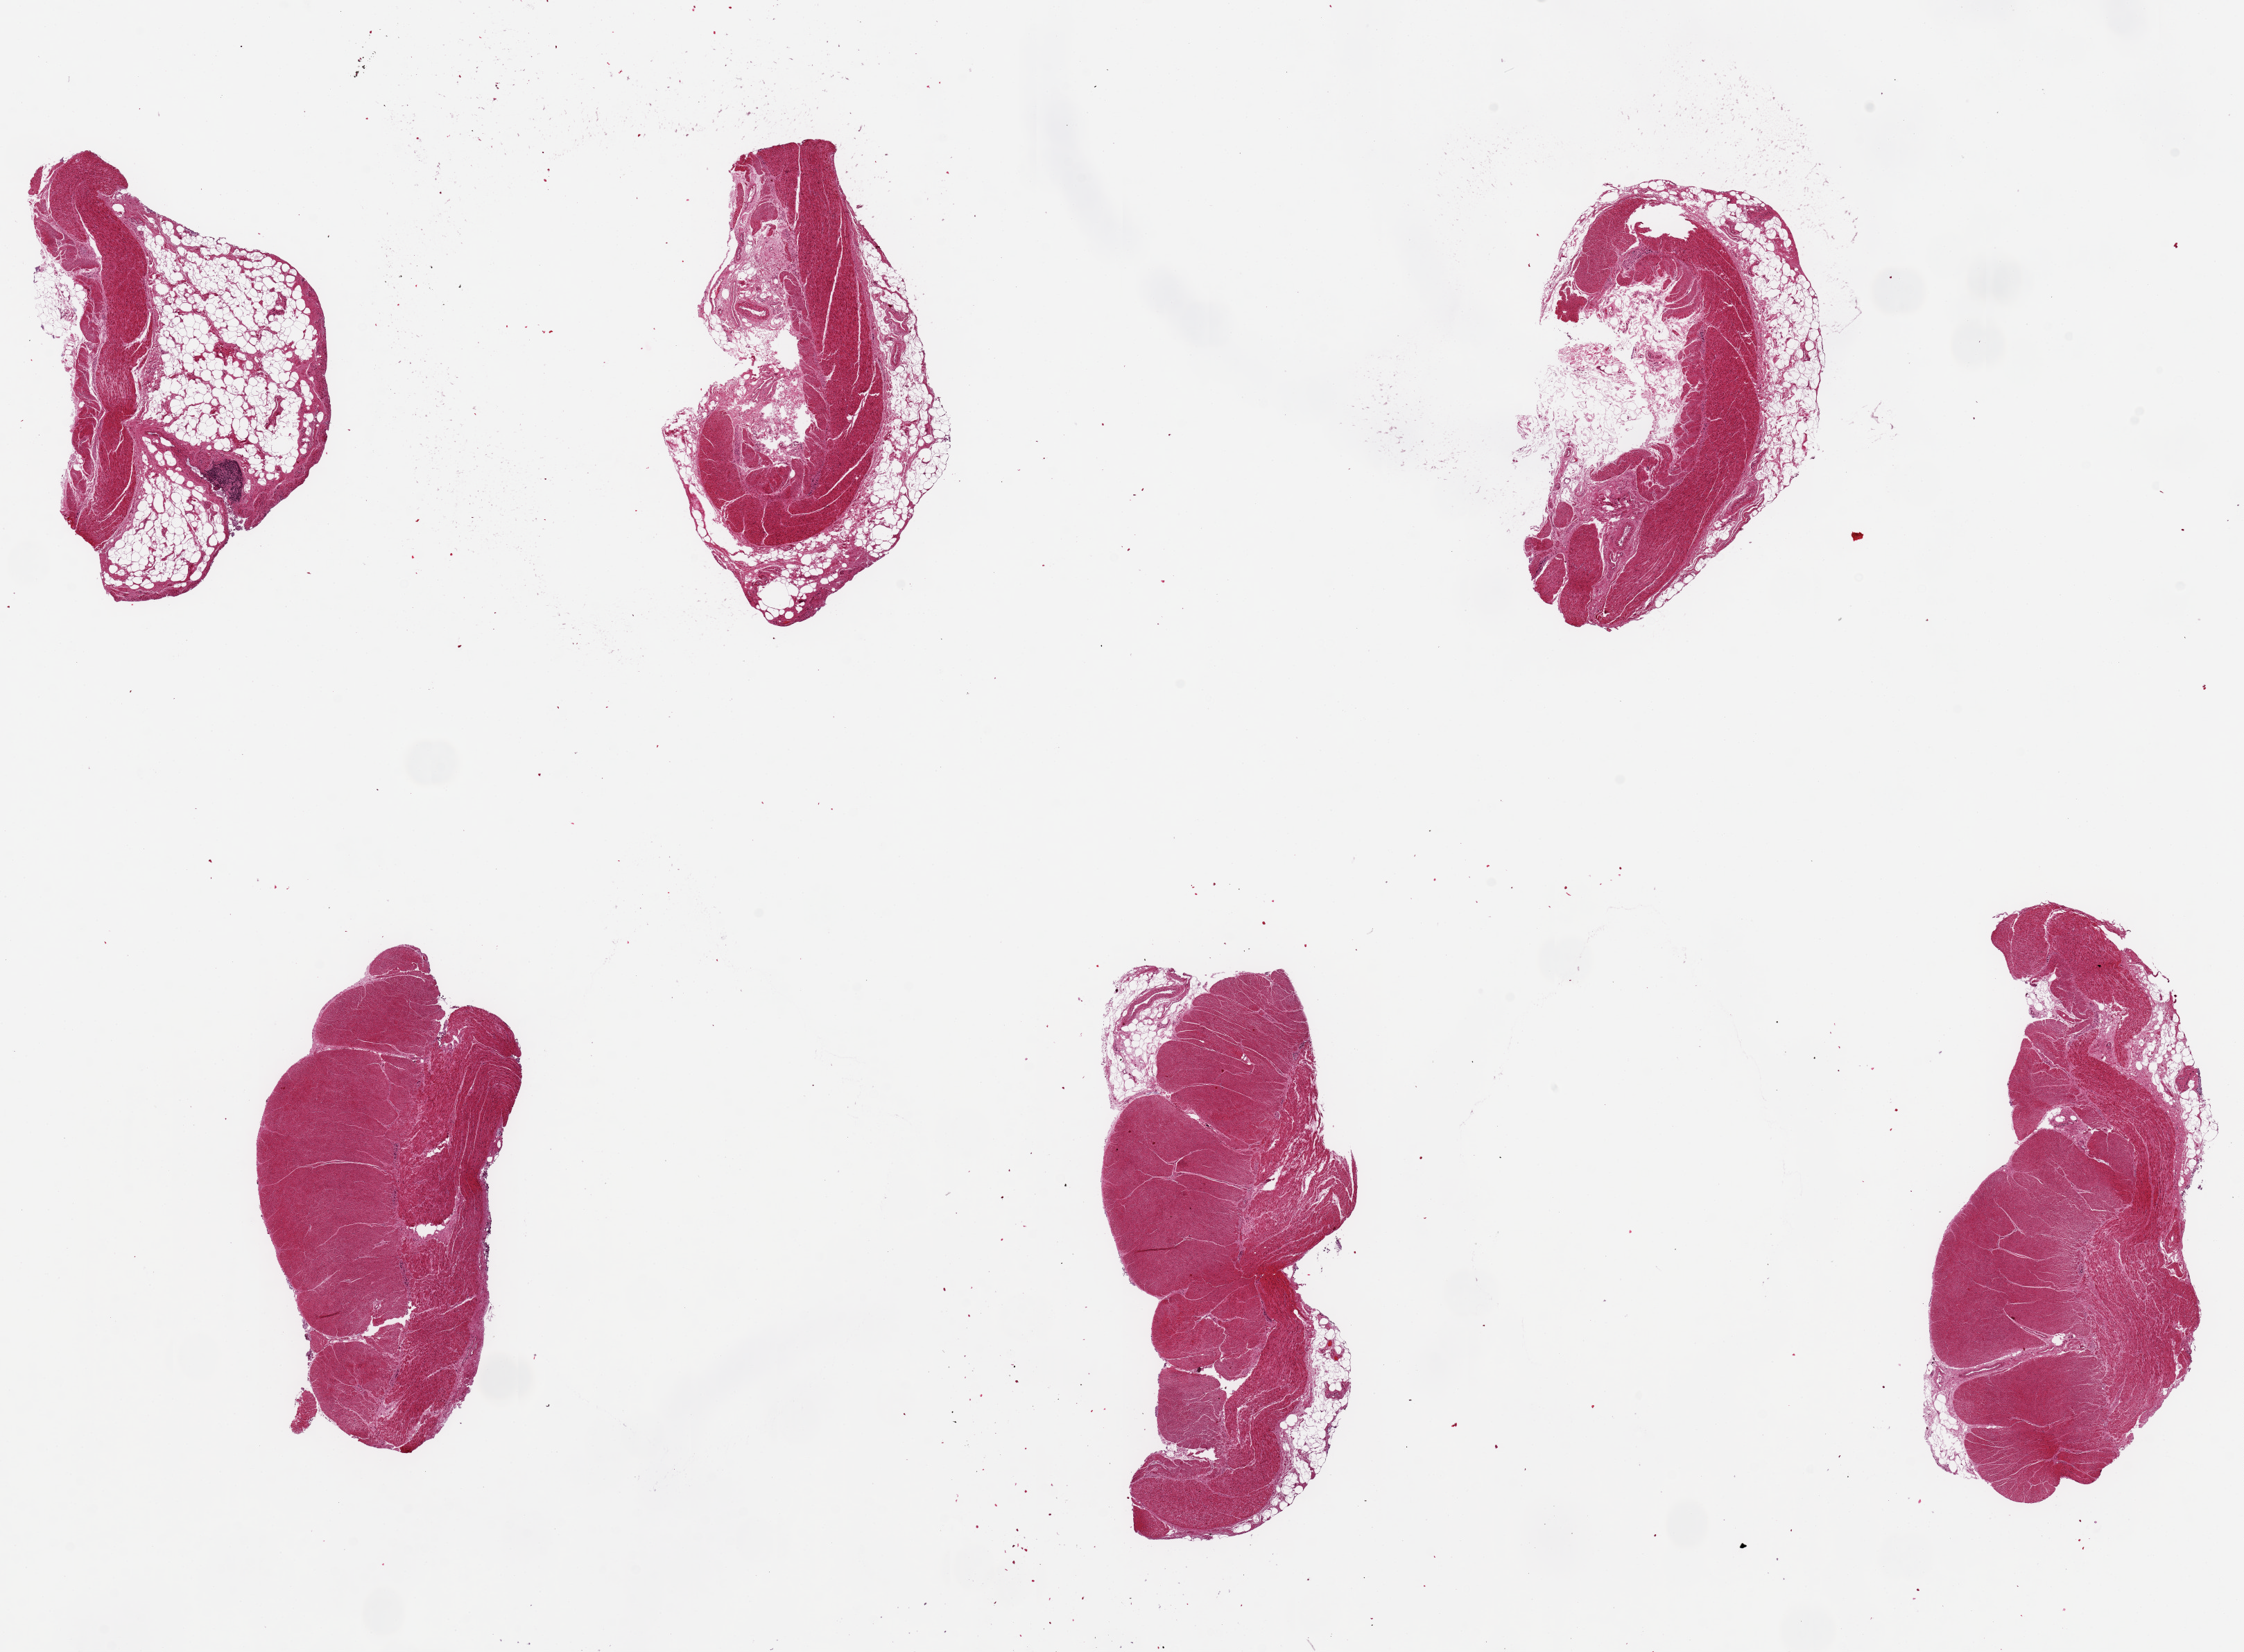
Whole-slide image, H&E stain — a low-resolution overview of the entire scanned area, about 25.6 x 18.8 mm; PAXgene-fixed paraffin-embedded (PFPE) section; target tissue: sigmoid colon; donor tissue sample. Donor: male.
• pathologist's review note for this sample: 6 pieces, up to 7x3mm